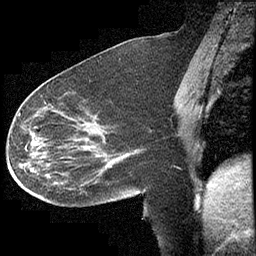
Breast MRI (dynamic contrast-enhanced), one sagittal slice; position 170 of 232 along the scan axis; dynamic contrast-enhanced study with each time point stored as its own series, time point 2 of 4 at this slice position (early post-contrast, ordered by acquisition time); 1.5 T; TE 4.2 ms, TR 6.7 ms; 3 mm slice thickness; 256 × 256 image matrix. Female patient, age 63 years. From the clinical record (not read from this slice): setting: breast cancer imaged before/during neoadjuvant chemotherapy; receptor status: triple-negative.
Outlined on this slice (semi-automatic segmentation, software-assisted and operator-edited):
- analysis volume of interest (the breast-tissue region the enhancement analysis was run in; not a lesion): bounding box (x1, y1, x2, y2) in pixels: (13, 90, 140, 208)
- tumour enhancement mask (voxels above the 70 % enhancement threshold inside the analysis volume of interest): (19, 113, 126, 158)